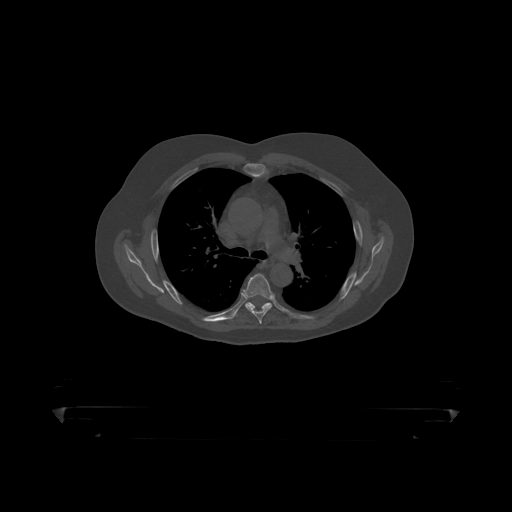
CT including the spine, one axial slice; slice 314 of 390 in the series (ordered by position); reconstruction kernel STANDARD; 120 kVp; bone window (W 1800 / L 400 HU); 1.25 mm slice thickness; 512 × 512 image matrix, field of view 650 × 650 mm. Patient: male, 60 years. Case-level facts recorded for this patient, not image findings: primary cancer: prostate.
Annotated regions visible in this slice (semi-automatically segmented with operator editing):
- T5 vertebra: bounding box (x1, y1, x2, y2) in pixels: (242, 274, 275, 319)
- T6 vertebra: (235, 302, 272, 316)